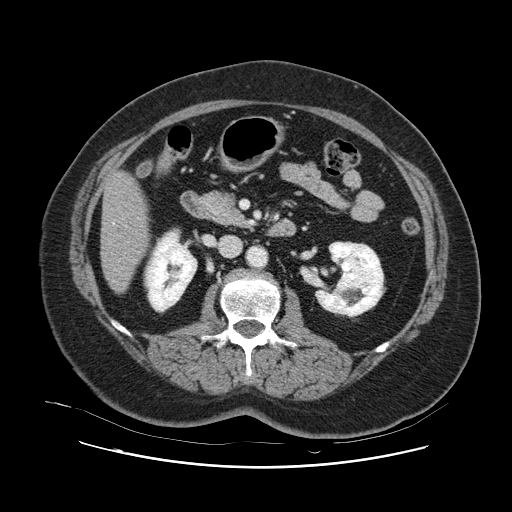
Contrast-enhanced abdominal CT, one axial slice; slice 32 of 132 in the series (ordered by position); 120 kVp; intravenous contrast given; soft-tissue window (W 400 / L 40 HU); 2.5 mm slice thickness; 512 × 512 image matrix. Female patient, age 73 years. From the clinical record (not read from this slice): diagnosis: colorectal cancer liver metastases, imaged before liver resection; multiple liver metastases: no; largest metastasis: 7 cm; disease in both lobes: no.
Outlined on this slice (manually delineated by an expert):
- hepatic veins: box from (x=112, y=223) to (x=115, y=226) px
- liver: (x=102, y=175)–(x=149, y=293)
- planned liver remnant (the part of the liver to remain after resection): (x=101, y=174)–(x=149, y=294)